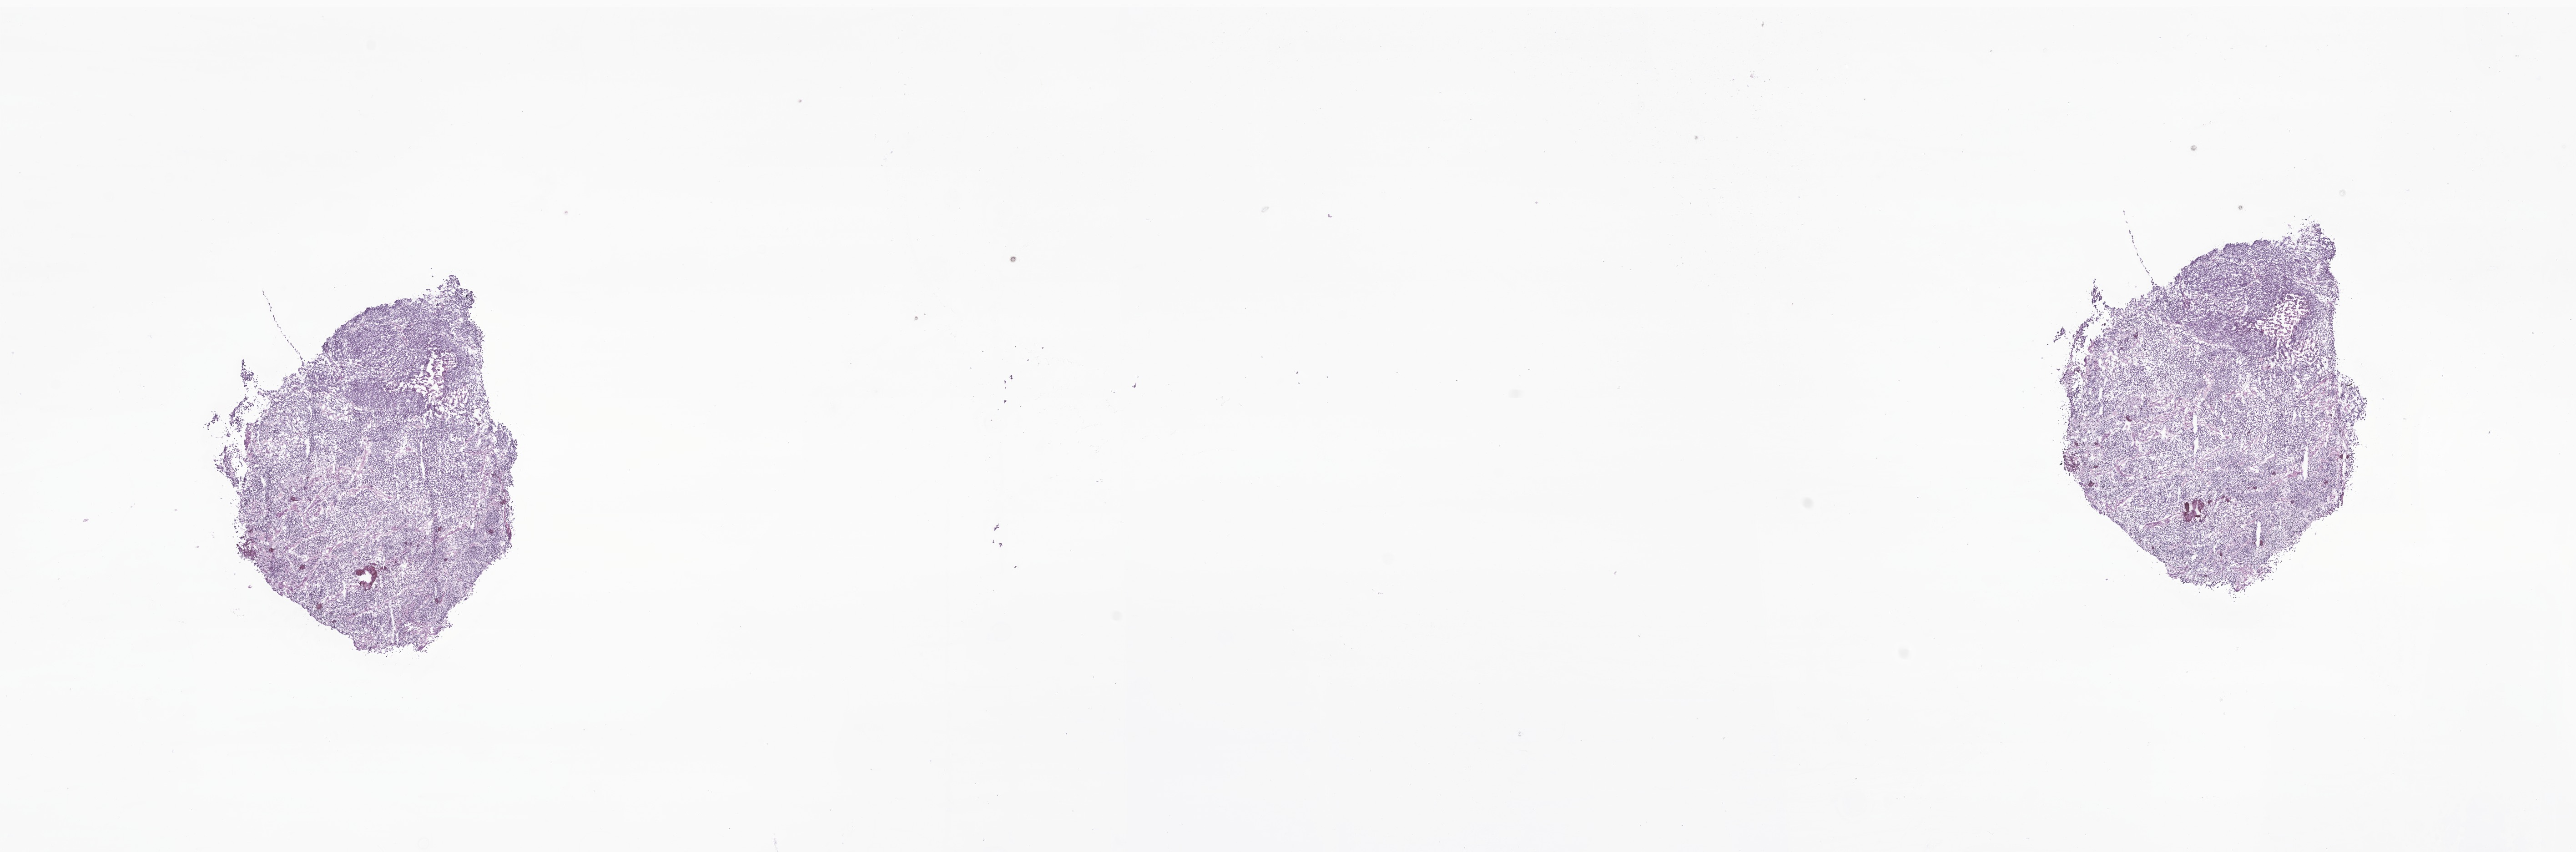
Whole-slide image, H&E stain of tumor tissue from the brain, low-resolution overview of the scanned area, about 23.9 x 7.9 mm, frozen section (OCT-embedded). Female patient, age 34 months (2 years 10 months).
Diagnosis (ICD-O-3 morphology term): Medulloblastoma, NOS.